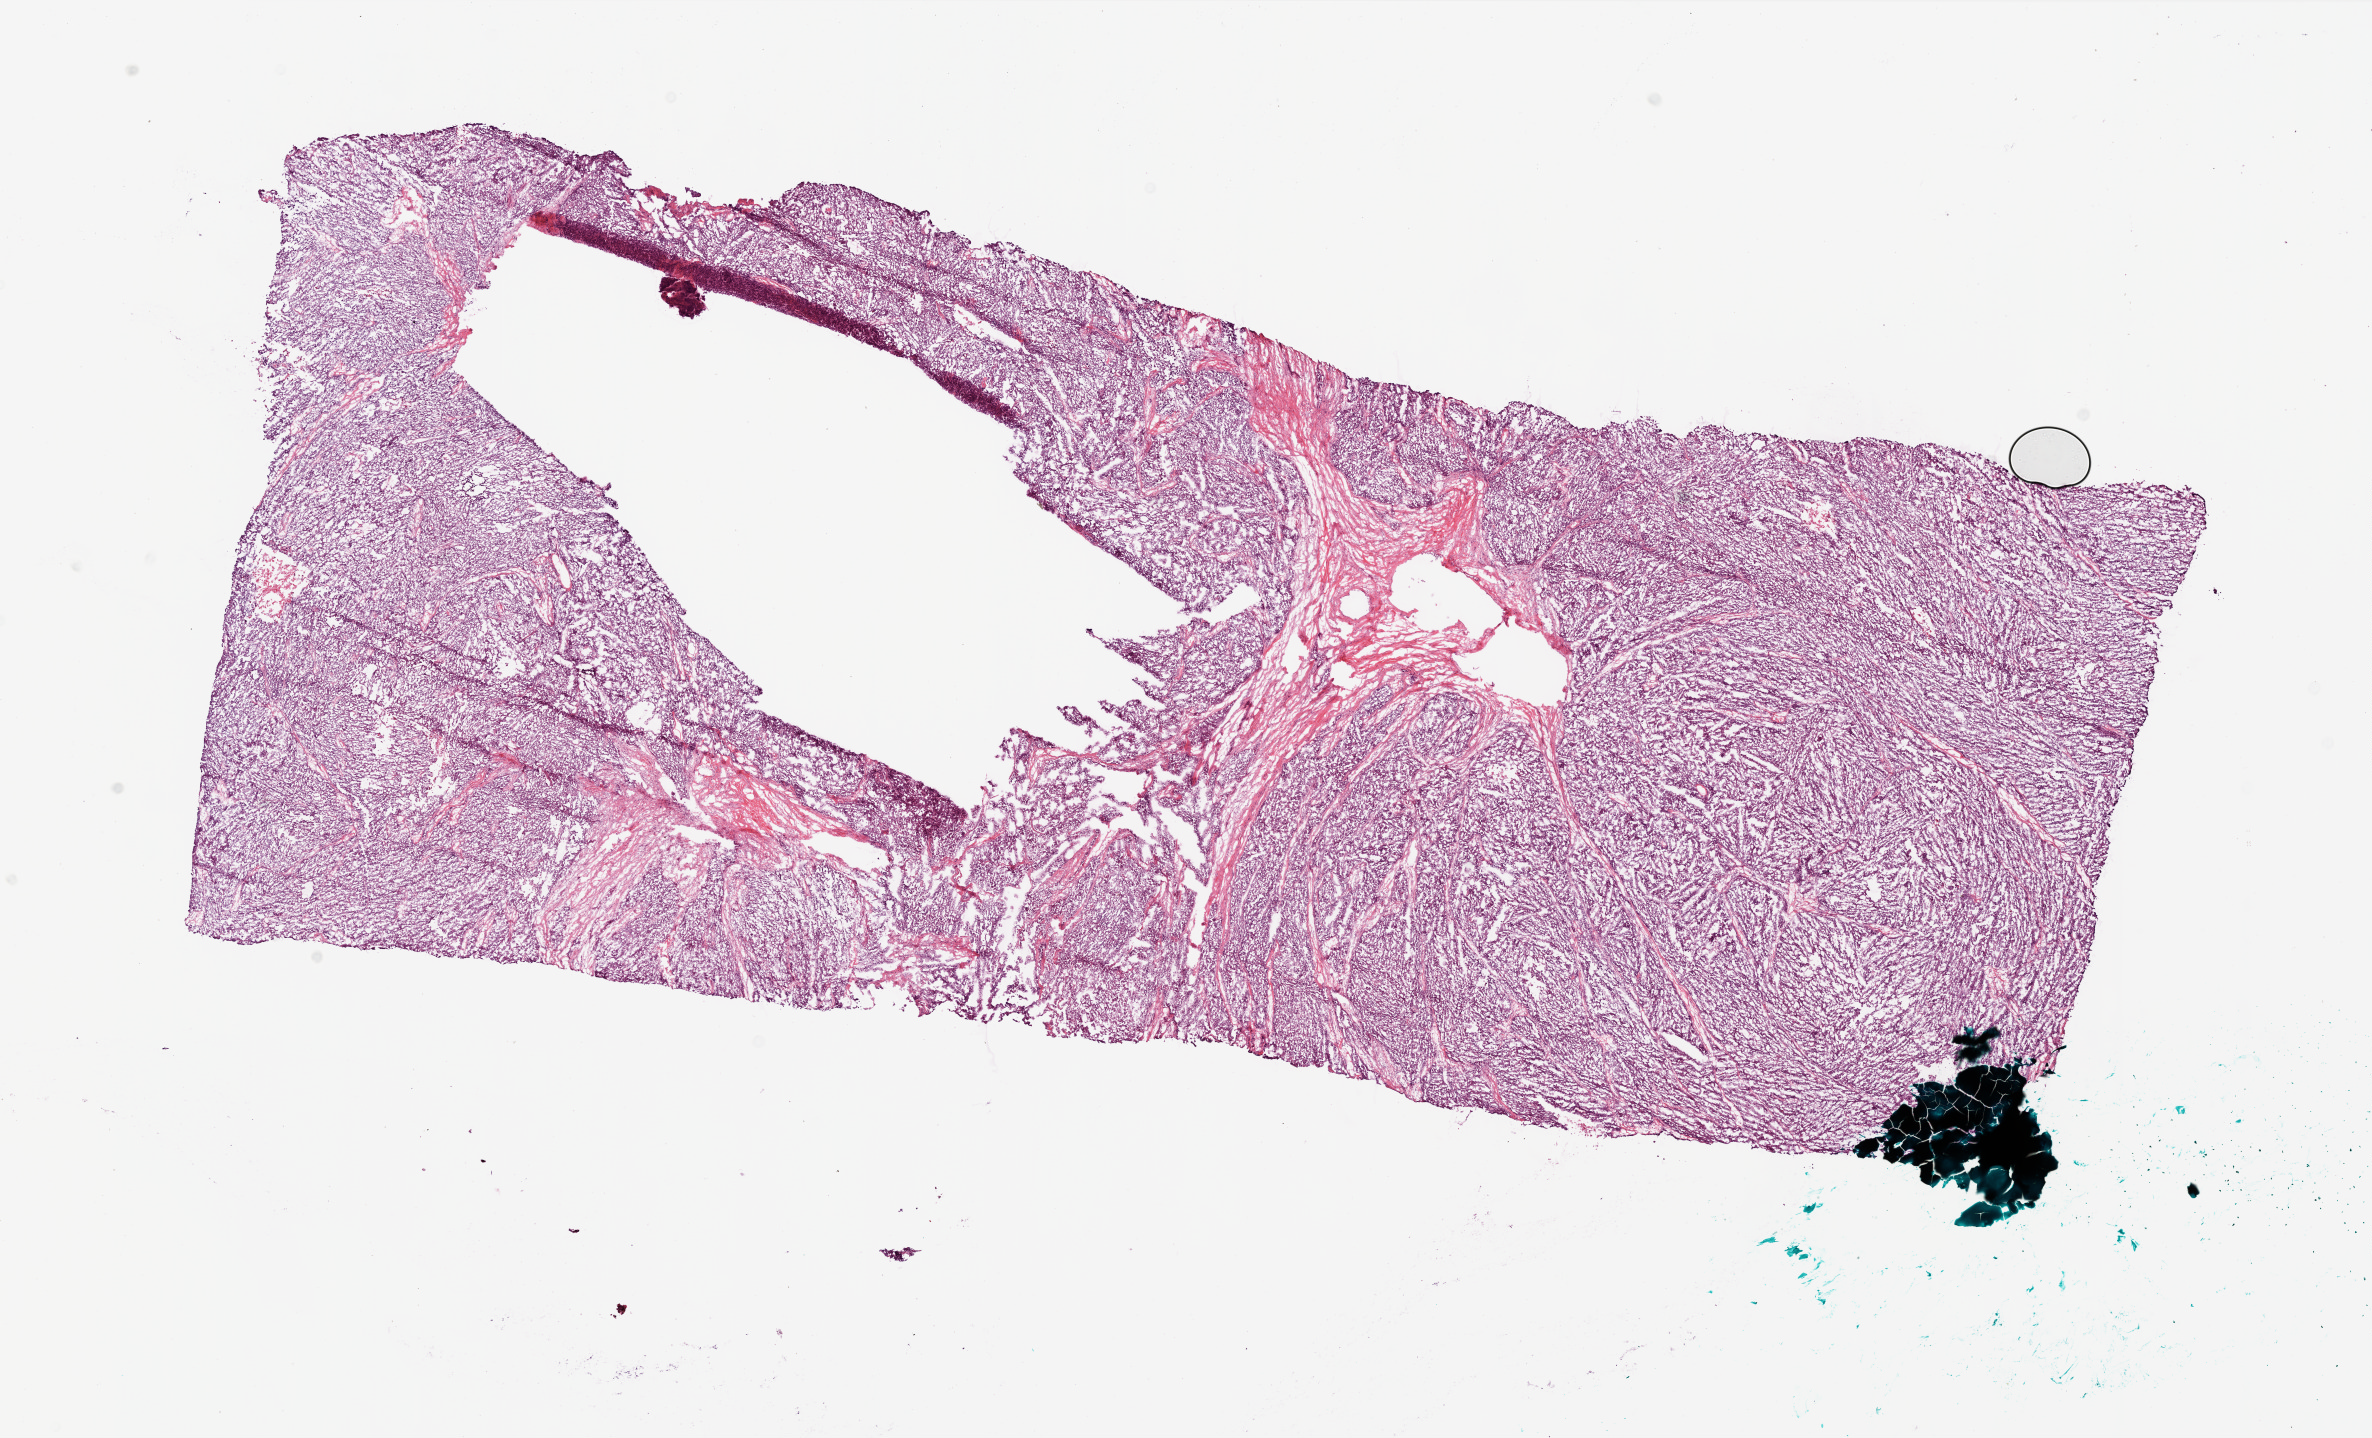
Whole-slide histology image, Hematoxylin and eosin (H&E) stained — shown as a low-resolution overview of the whole scanned area (about 19.0 x 11.5 mm, from a 20x scan), frozen section, ovary, primary tumour sample. Patient: female, age at initial diagnosis 63 years. Histologic grade: G3 (poorly differentiated). Pathologist review of this section (percent, as recorded): tumour cells 88%, tumour nuclei 89%, normal cells 10%, stromal cells 1%, necrosis 1%.
• FIGO stage: IIIC
• histologic diagnosis: Serous cystadenocarcinoma, NOS